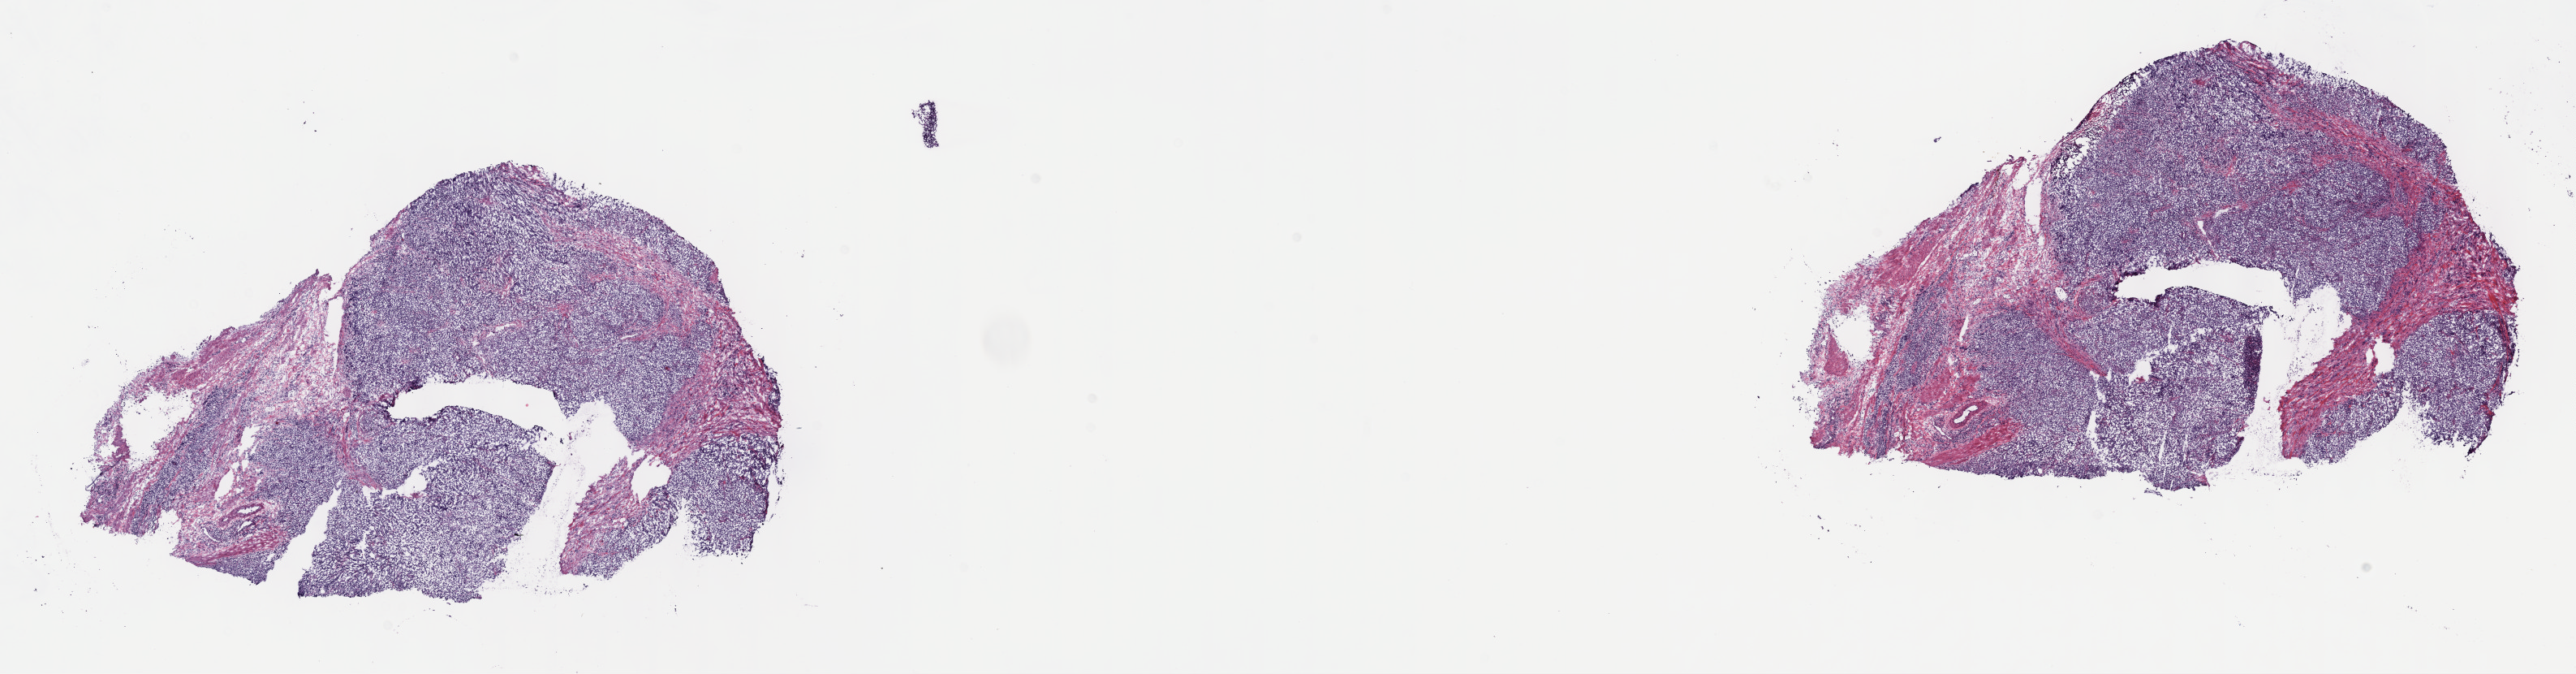
Digitized Hematoxylin and eosin (H&E) stained tissue section (whole slide) — low-resolution overview of the scanned area, about 25.7 x 6.7 mm (from a 40x scan). Frozen section from the top of the tissue portion. Testis, additional new primary tumour sample. Patient: male, age at initial diagnosis 30 years. Slide review estimates, as recorded: tumour cells 100%, tumour nuclei 75%, normal cells 0%, stromal cells 0%, necrosis 0%. Infiltration values recorded for this section: lymphocyte infiltration 2%, monocyte infiltration 0%, neutrophil infiltration 0%.
This section: additional new primary tumour. Patient diagnosis: Seminoma, NOS.